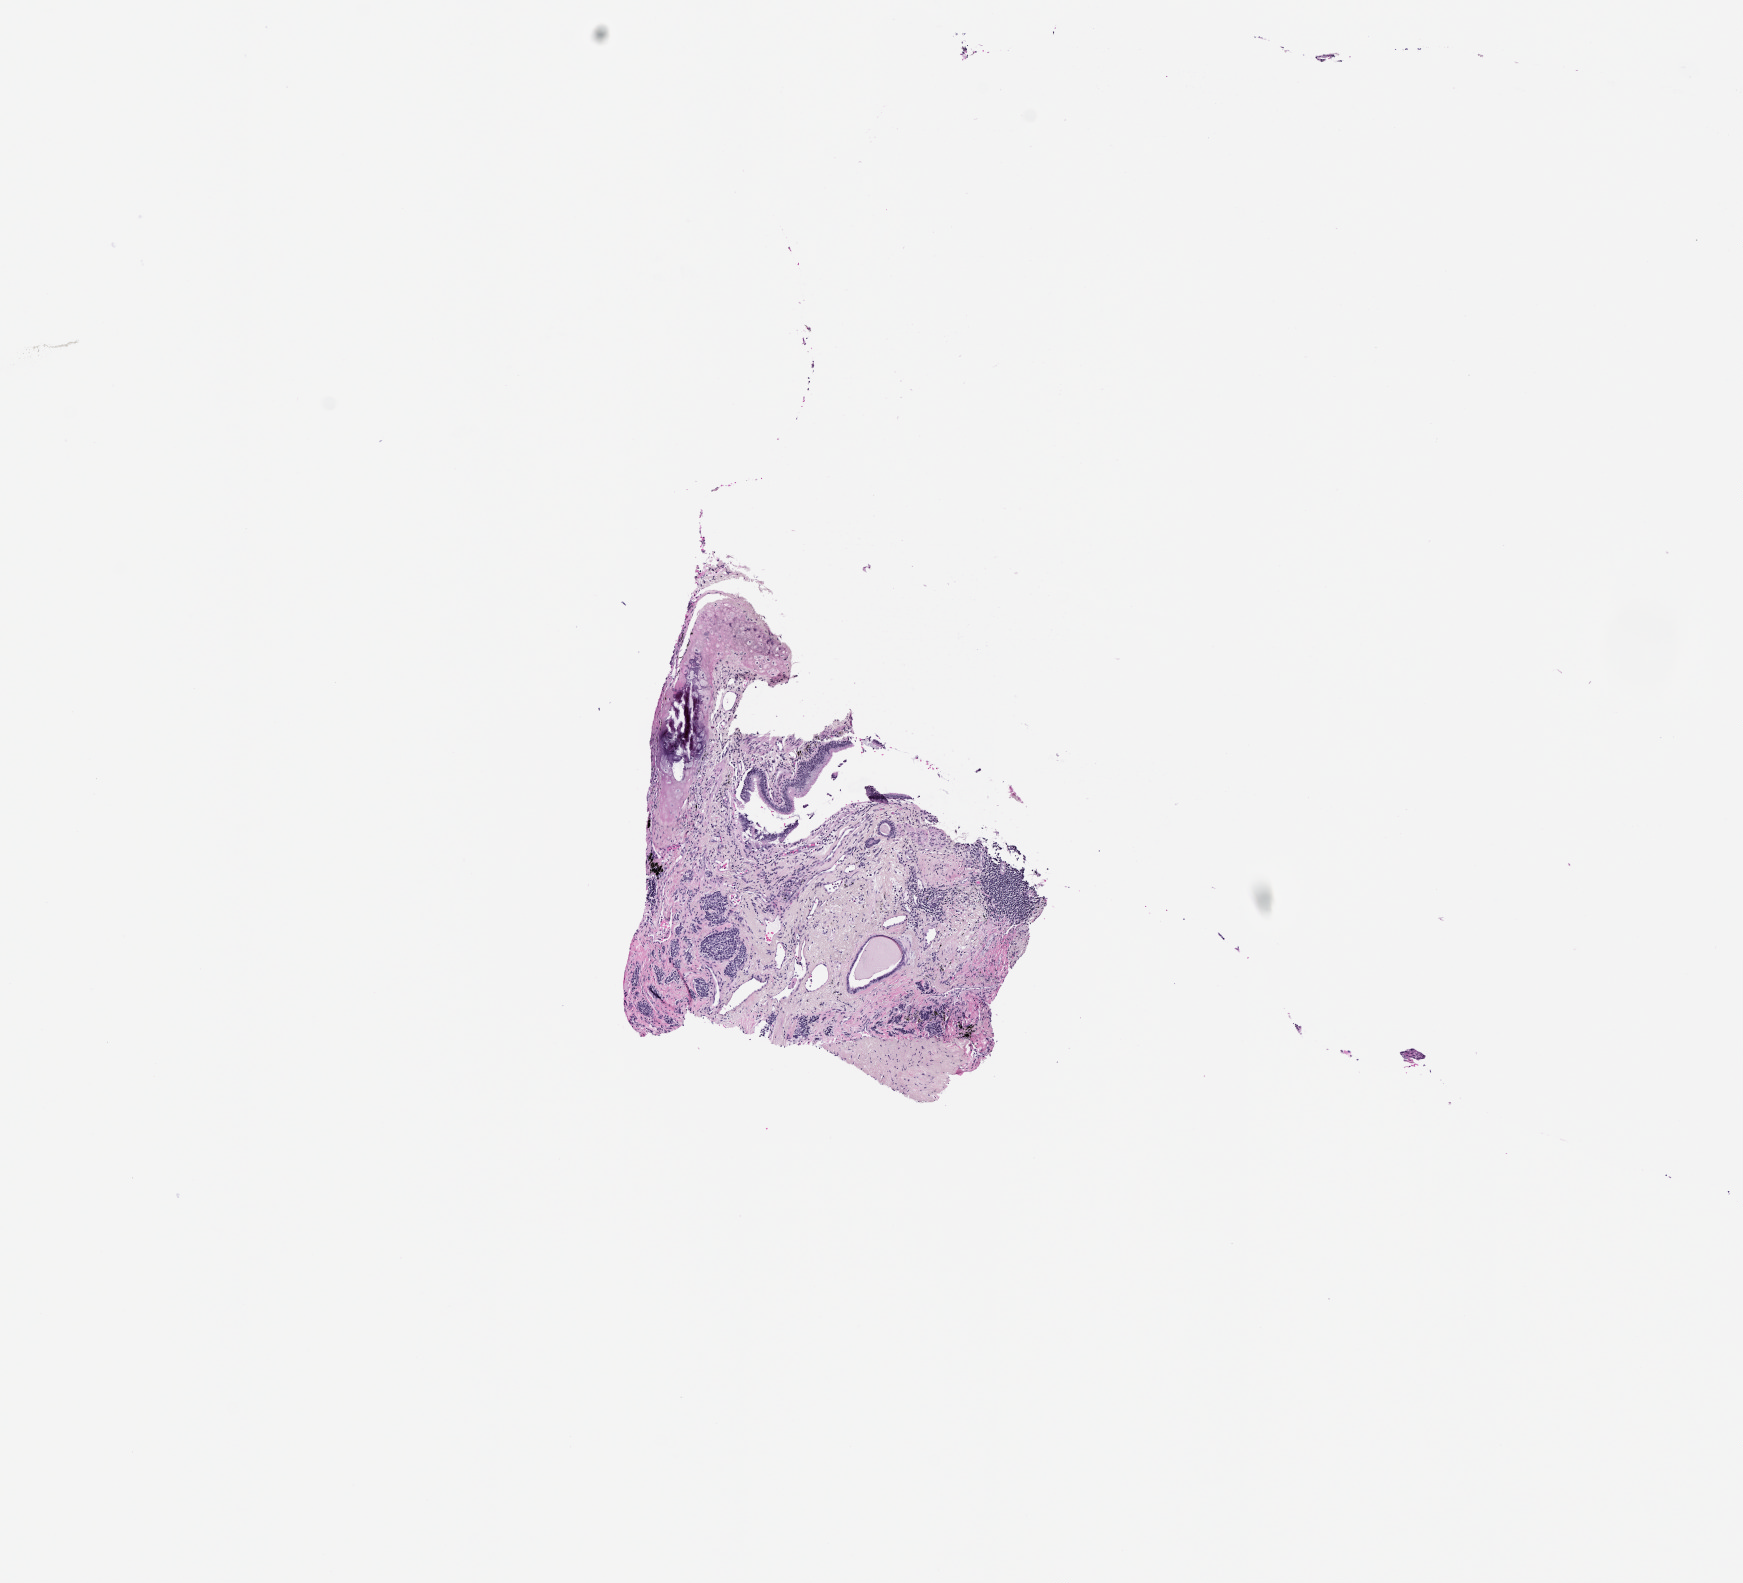
Whole-slide histology image, H&E-stained, whole scanned area (about 7.0 x 6.4 mm) shown as a low-resolution overview. Tumour tissue sample, lung. Patient sex: female.
- patient diagnosis (cohort enrolment): squamous cell carcinoma (lung)